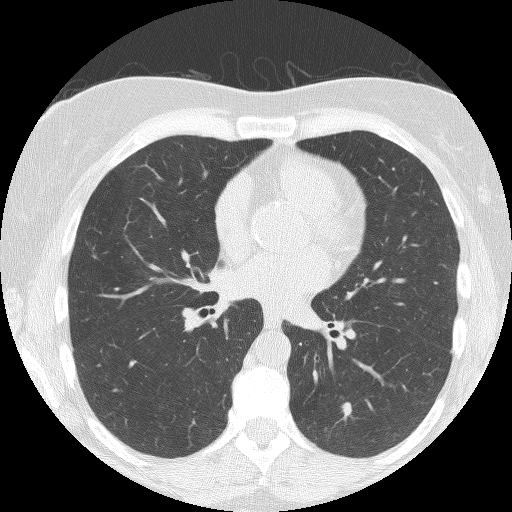
Low-dose screening chest CT, axial slice; second annual screen; lung window (W 1500 / L -600 HU); 2.5 mm slice thickness; lung (sharp) reconstruction kernel (BONE); slice 74 of 150 in the series. Female, age 60 years at enrolment. Former smoker at enrolment.
Lesion marked by an expert reader, bounding box (x1, y1, x2, y2) in pixels: (322, 384, 359, 426). Reader record for this screening exam (exam-level; its link to the box is not recorded): non-calcified nodule or mass ≥4 mm, left lower lobe, 16 × 7 mm, smooth margins, soft tissue attenuation, pre-existing on the prior screen: no. Later outcome: lung cancer diagnosed 54 days after this screen — small cell carcinoma, NOS, left lower lobe, stage IIA (AJCC 6th edition), 12 mm at pathology.